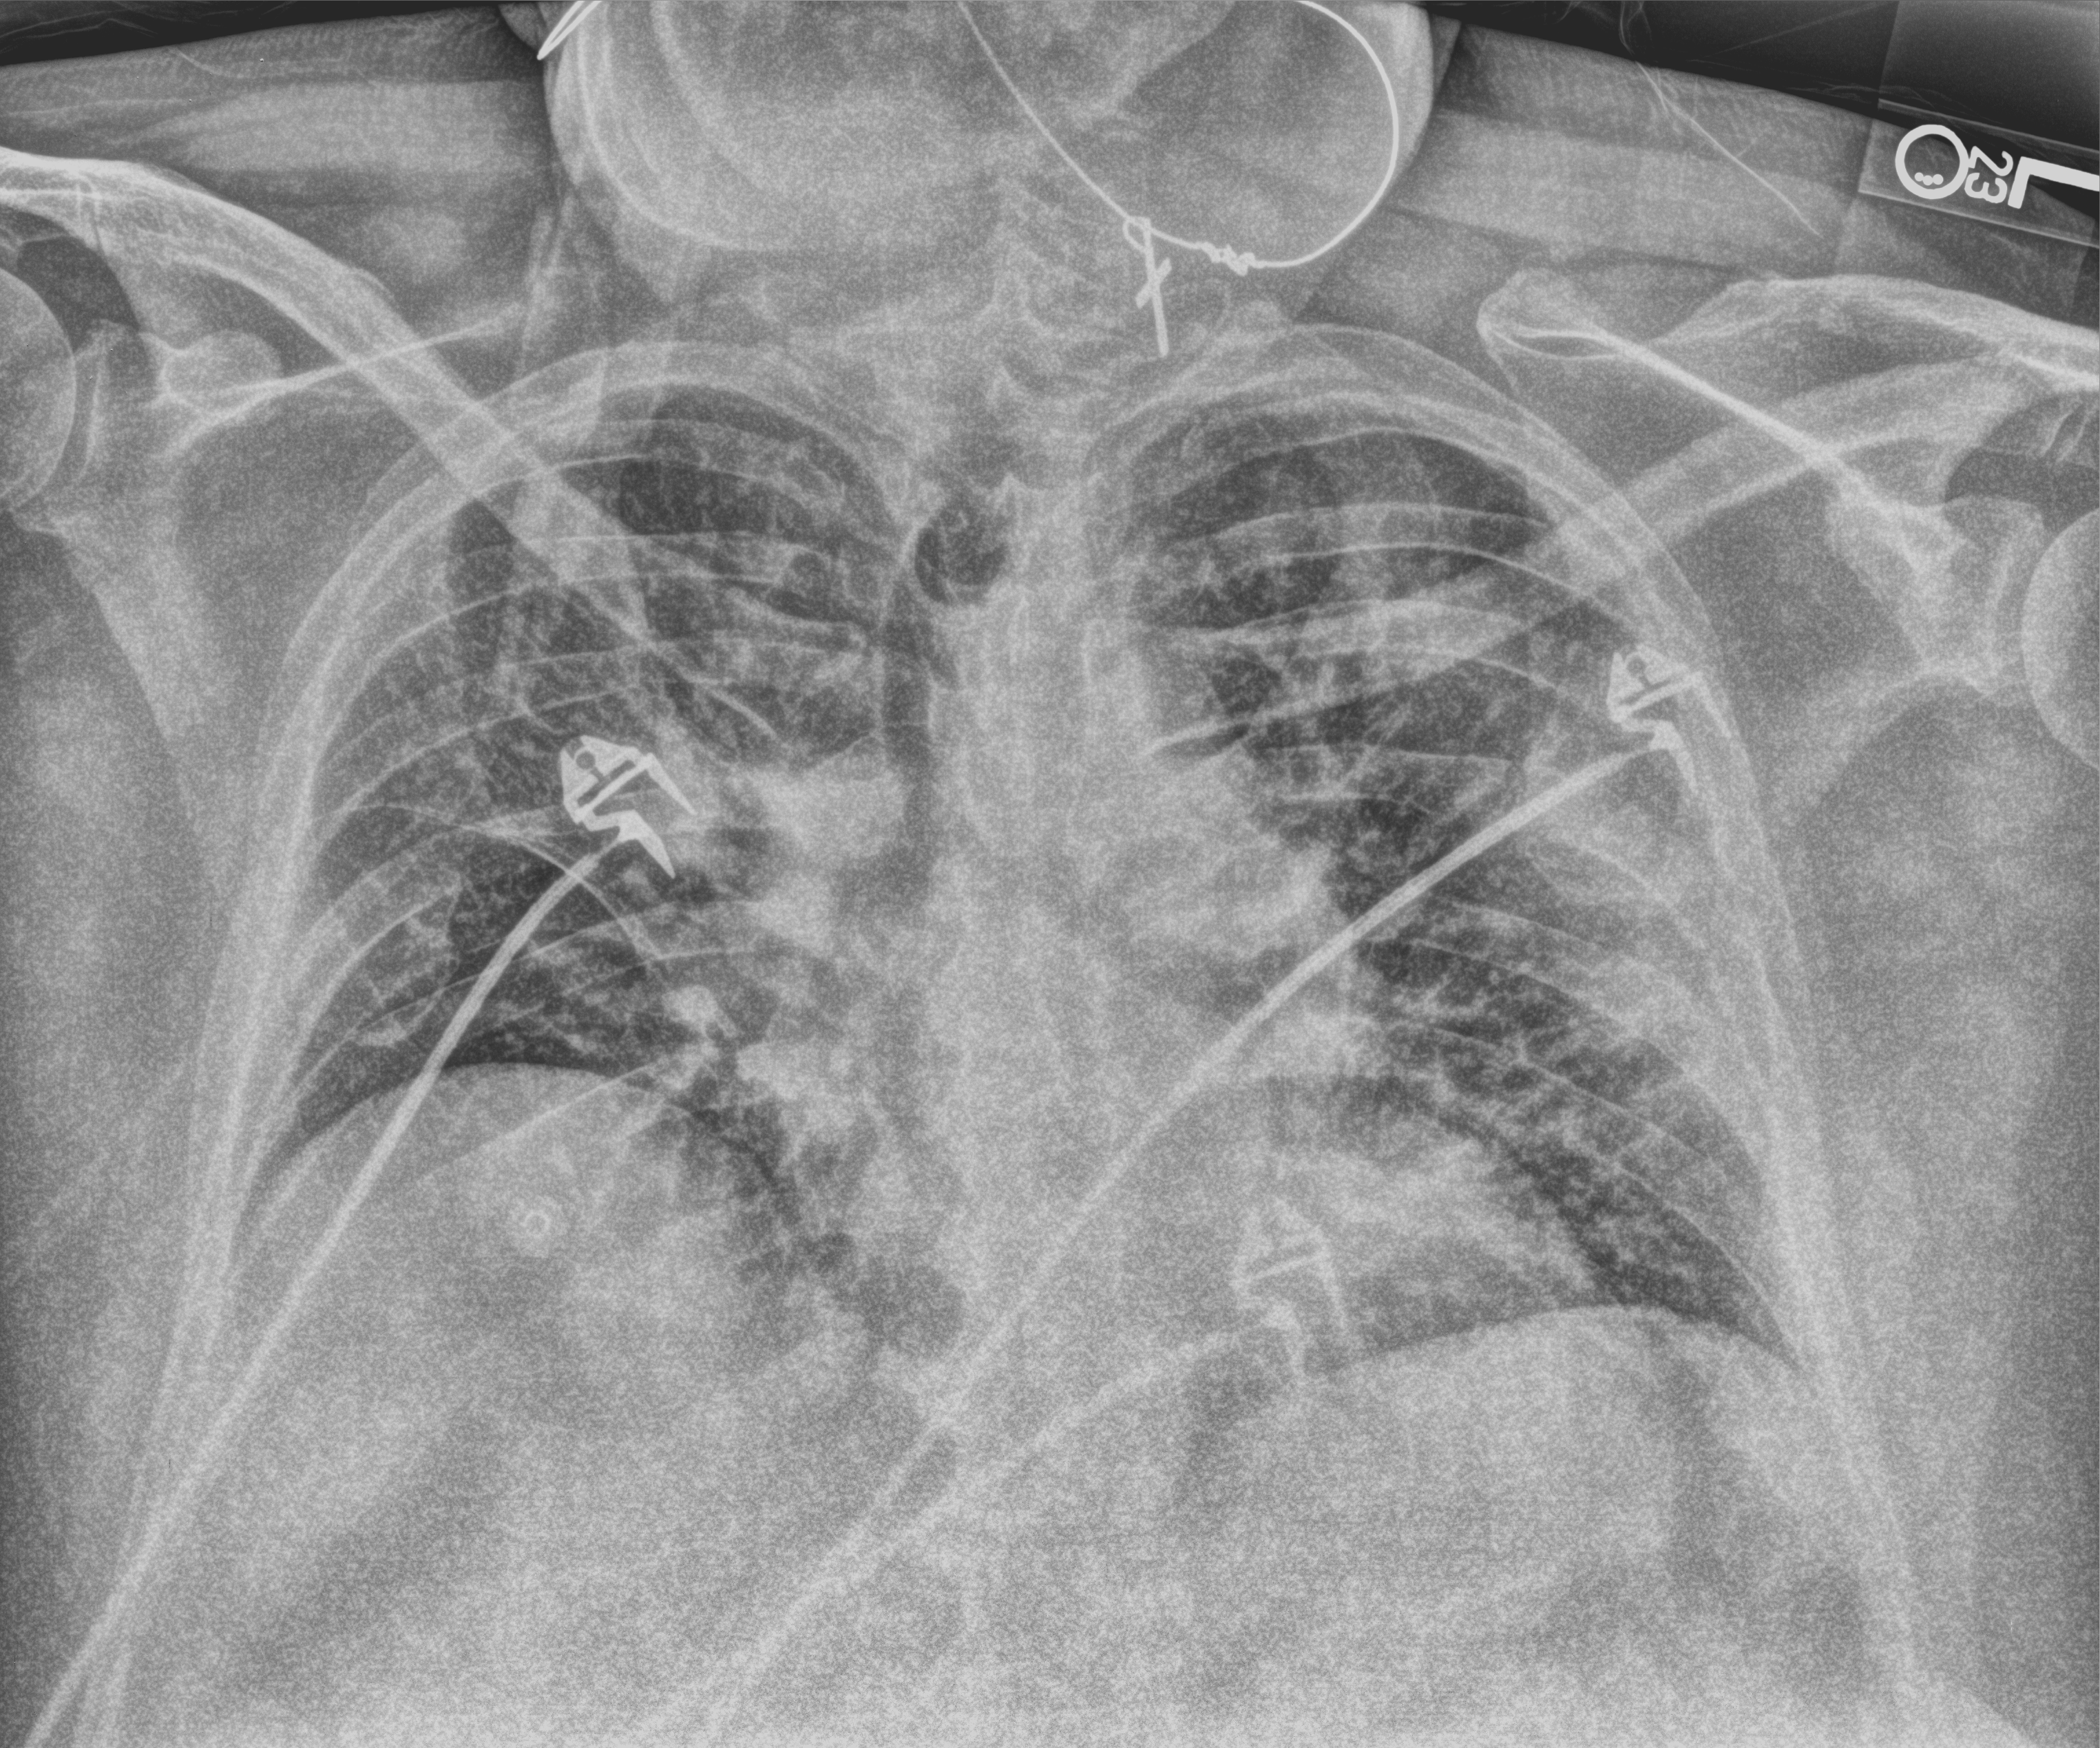
Portable chest radiograph, anteroposterior (AP) projection. Male patient hospitalised with COVID-19, age 60–74 years.
From the hospital-stay record, not from the radiograph (when in the stay this image was taken is not recorded):
- admitted to intensive care during this hospital stay: no
- mechanically ventilated during this hospital stay: no
- length of hospital stay: 11 days